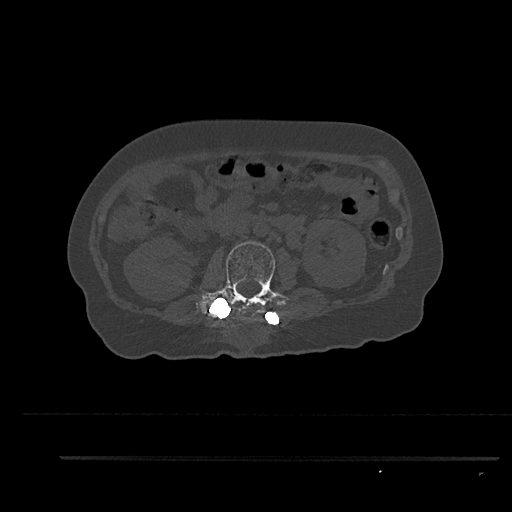
CT including the spine, one axial slice; position 156 of 797 along the scan axis; reconstruction kernel Br40s/3; 120 kVp; bone window (W 1800 / L 400 HU); 0.5 mm slice thickness; 512 × 512 image matrix, field of view 408 × 408 mm. Patient: female, 44 years. From the clinical record (not read from this slice): primary cancer: renal; vertebrae with lytic lesions (as recorded): L1.
Outlined on this slice (semi-automatically segmented with operator editing):
- L2 vertebra: bounding box <196,241,284,320> (left, top, right, bottom; pixels)